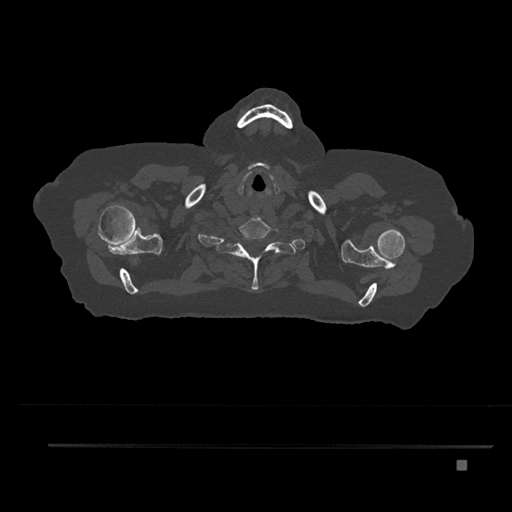
CT including the spine, one axial slice; slice 707 of 797 in the series (ordered by position); 120 kVp; bone window (W 1800 / L 400 HU); 0.5 mm slice thickness; 512 × 512 image matrix, field of view 437 × 437 mm. Patient: female, 76 years. Case-level facts recorded for this patient, not image findings: primary cancer: lung; vertebrae with lytic lesions (as recorded): T11, L3.
Structures marked on this image (semi-automatic segmentation, software-assisted and operator-edited):
- T1 vertebra: bounding box [x1, y1, x2, y2] px = [224, 234, 283, 291]